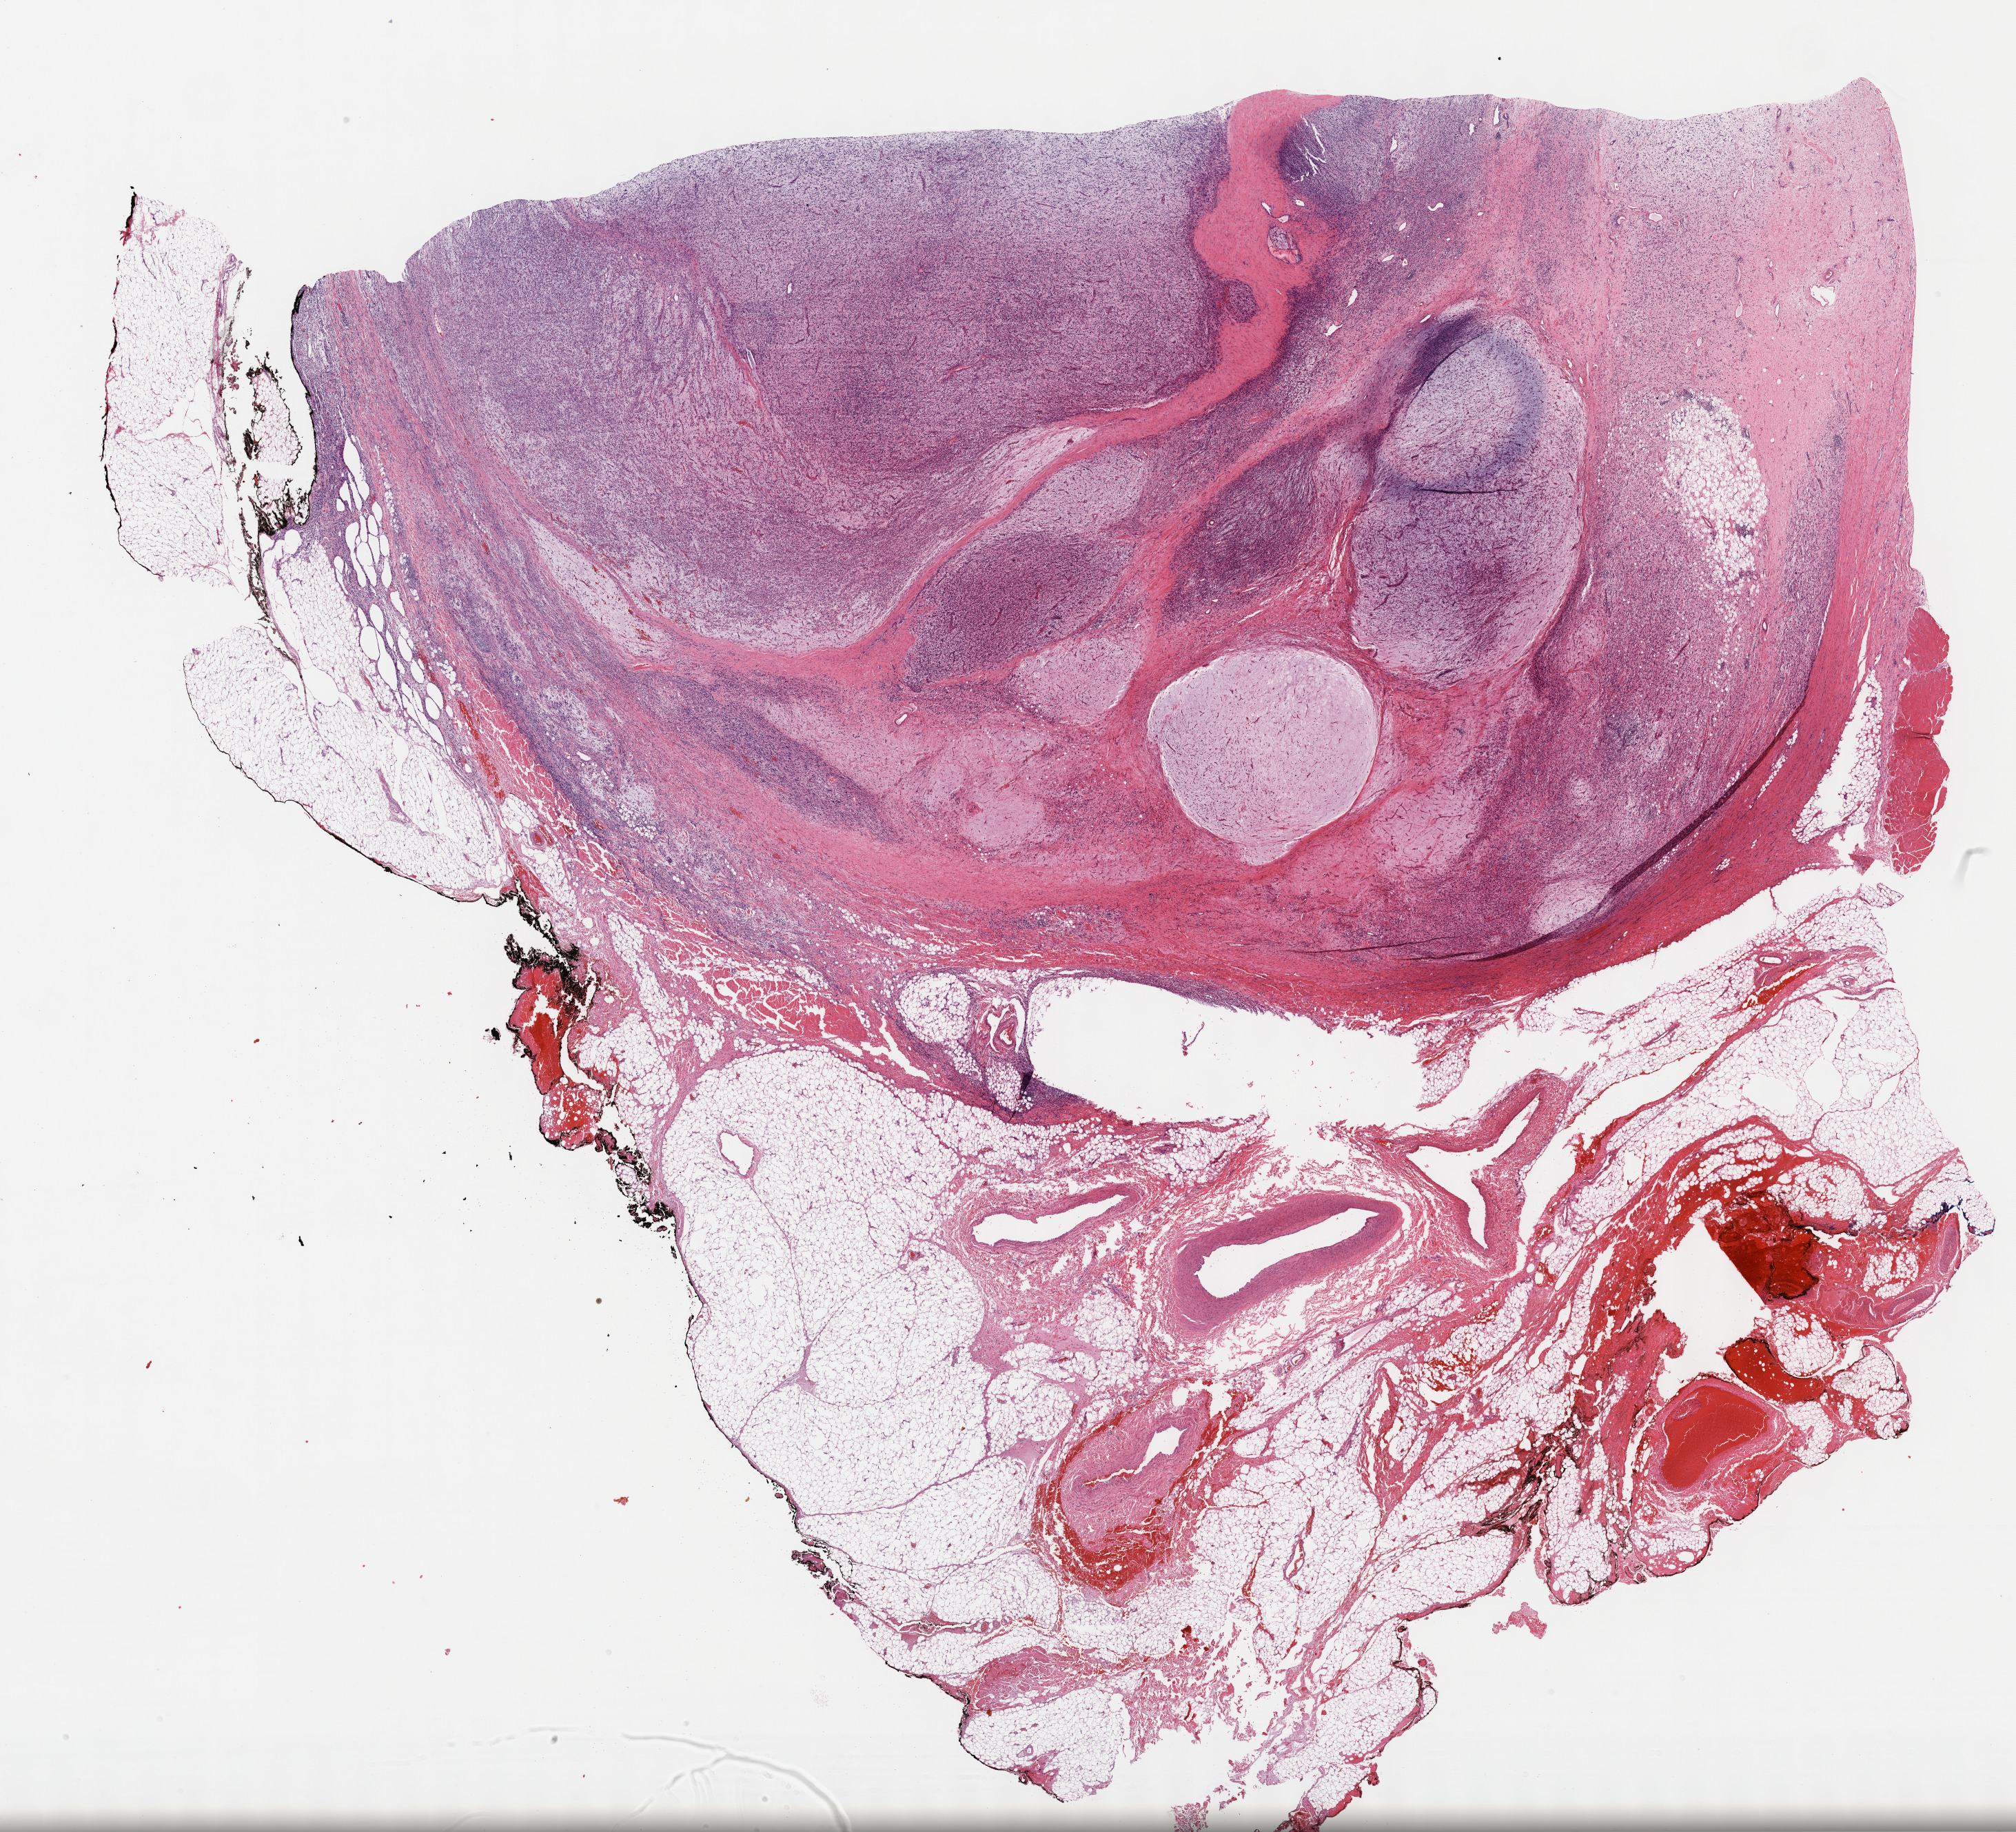
H&E-stained whole-slide image, a low-resolution overview of the entire scanned area, about 23.7 x 21.5 mm. FFPE section. Connective, subcutaneous and other soft tissues, primary tumour sample. Patient: male, age at initial diagnosis 35 years.
Diagnosis: Fibromyxosarcoma (connective, subcutaneous and other soft tissues of lower limb and hip).